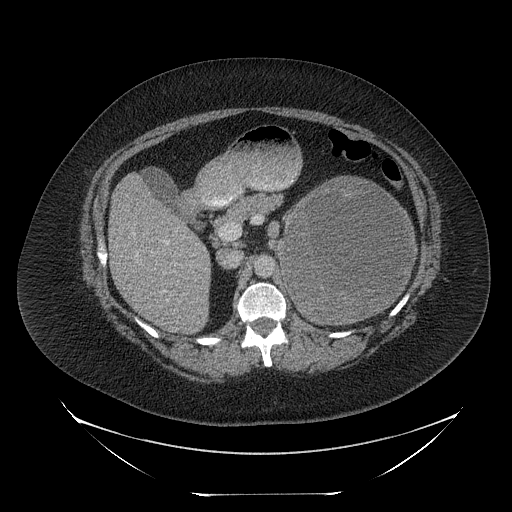
Contrast-enhanced abdominal CT, one axial slice. Slice 141 of 205 in the series (ordered by position). Intravenous contrast given. Soft-tissue window (W 400 / L 40 HU). 2.5 mm slice thickness. 512 × 512 image matrix. Female patient, age 53 years. From the clinical record (not read from this slice): diagnosis: adrenocortical carcinoma; tumour side: left adrenal; tumour size at pathology: 17 cm; Ki-67 index: 20 %; stage (as recorded): 3.
Annotated regions visible in this slice (semi-automatic segmentation, software-assisted and operator-edited):
- mass: bounding box <282,179,412,320> (left, top, right, bottom; pixels)